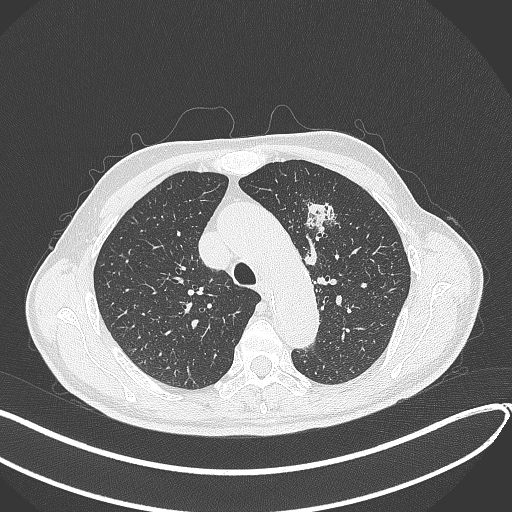
Chest CT, one axial slice; slice 305 of 459 in the series (ordered by position); lung window (W 1500 / L -600 HU); 1 mm slice thickness; 512 × 512 image matrix, field of view 400 × 400 mm. Male patient, age 74 years. Case-level facts recorded for this patient, not image findings: clinical TNM (as recorded): T2b N0 M1c.
Outlined on this slice (bounding box drawn by a radiologist):
- lung tumour (recorded histology: adenocarcinoma): bounding box (x1, y1, x2, y2) in pixels: (303, 199, 340, 246)